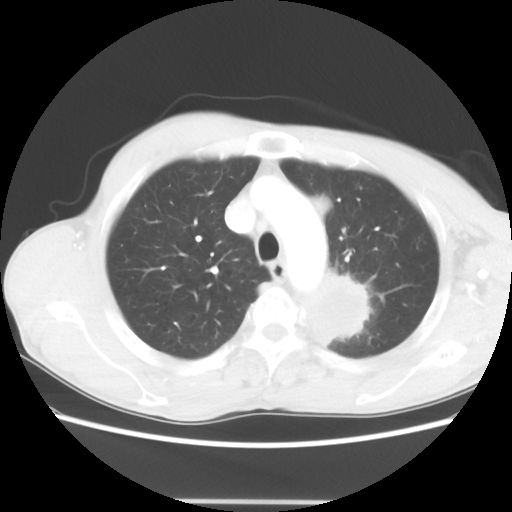
Chest CT, one axial slice; position 50 of 62 along the scan axis; reconstruction kernel STANDARD; lung window (W 1500 / L -600 HU); 5 mm slice thickness; 512 × 512 image matrix, field of view 360 × 360 mm. Male patient, age 61 years. From the clinical record (not read from this slice): clinical TNM (as recorded): T3 N1 M1.
Outlined on this slice (rectangle marked by the reading radiologist):
- lung tumour (recorded histology: adenocarcinoma): bounding box [x1, y1, x2, y2] px = [304, 264, 367, 350]
- lung tumour (recorded histology: adenocarcinoma): [310, 195, 334, 218]